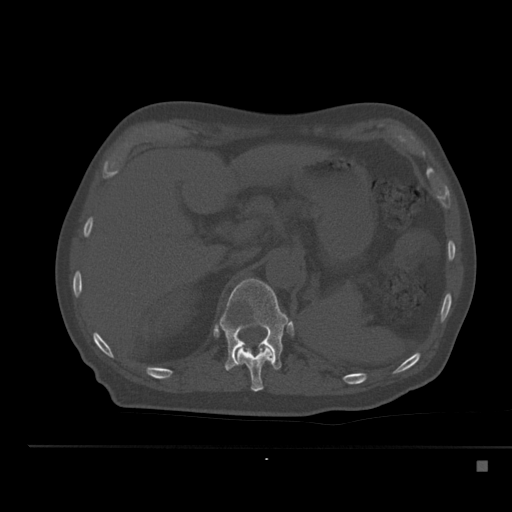
CT including the spine, one axial slice. Slice 236 of 517 in the series (ordered by position). Reconstruction kernel Br40s. 120 kVp. Bone window (W 1800 / L 400 HU). 1.5 mm slice thickness. 512 × 512 image matrix, field of view 408 × 408 mm. Patient: male, 70 years. Case-level facts recorded for this patient, not image findings: primary cancer: renal; vertebrae with lytic lesions (as recorded): T4, T6, T10, T12, L3, L4, L5.
Outlined on this slice (semi-automatically segmented with operator editing):
- T11 vertebra: box from (x=235, y=344) to (x=273, y=392) px
- T12 vertebra: (x=217, y=278)–(x=290, y=370)